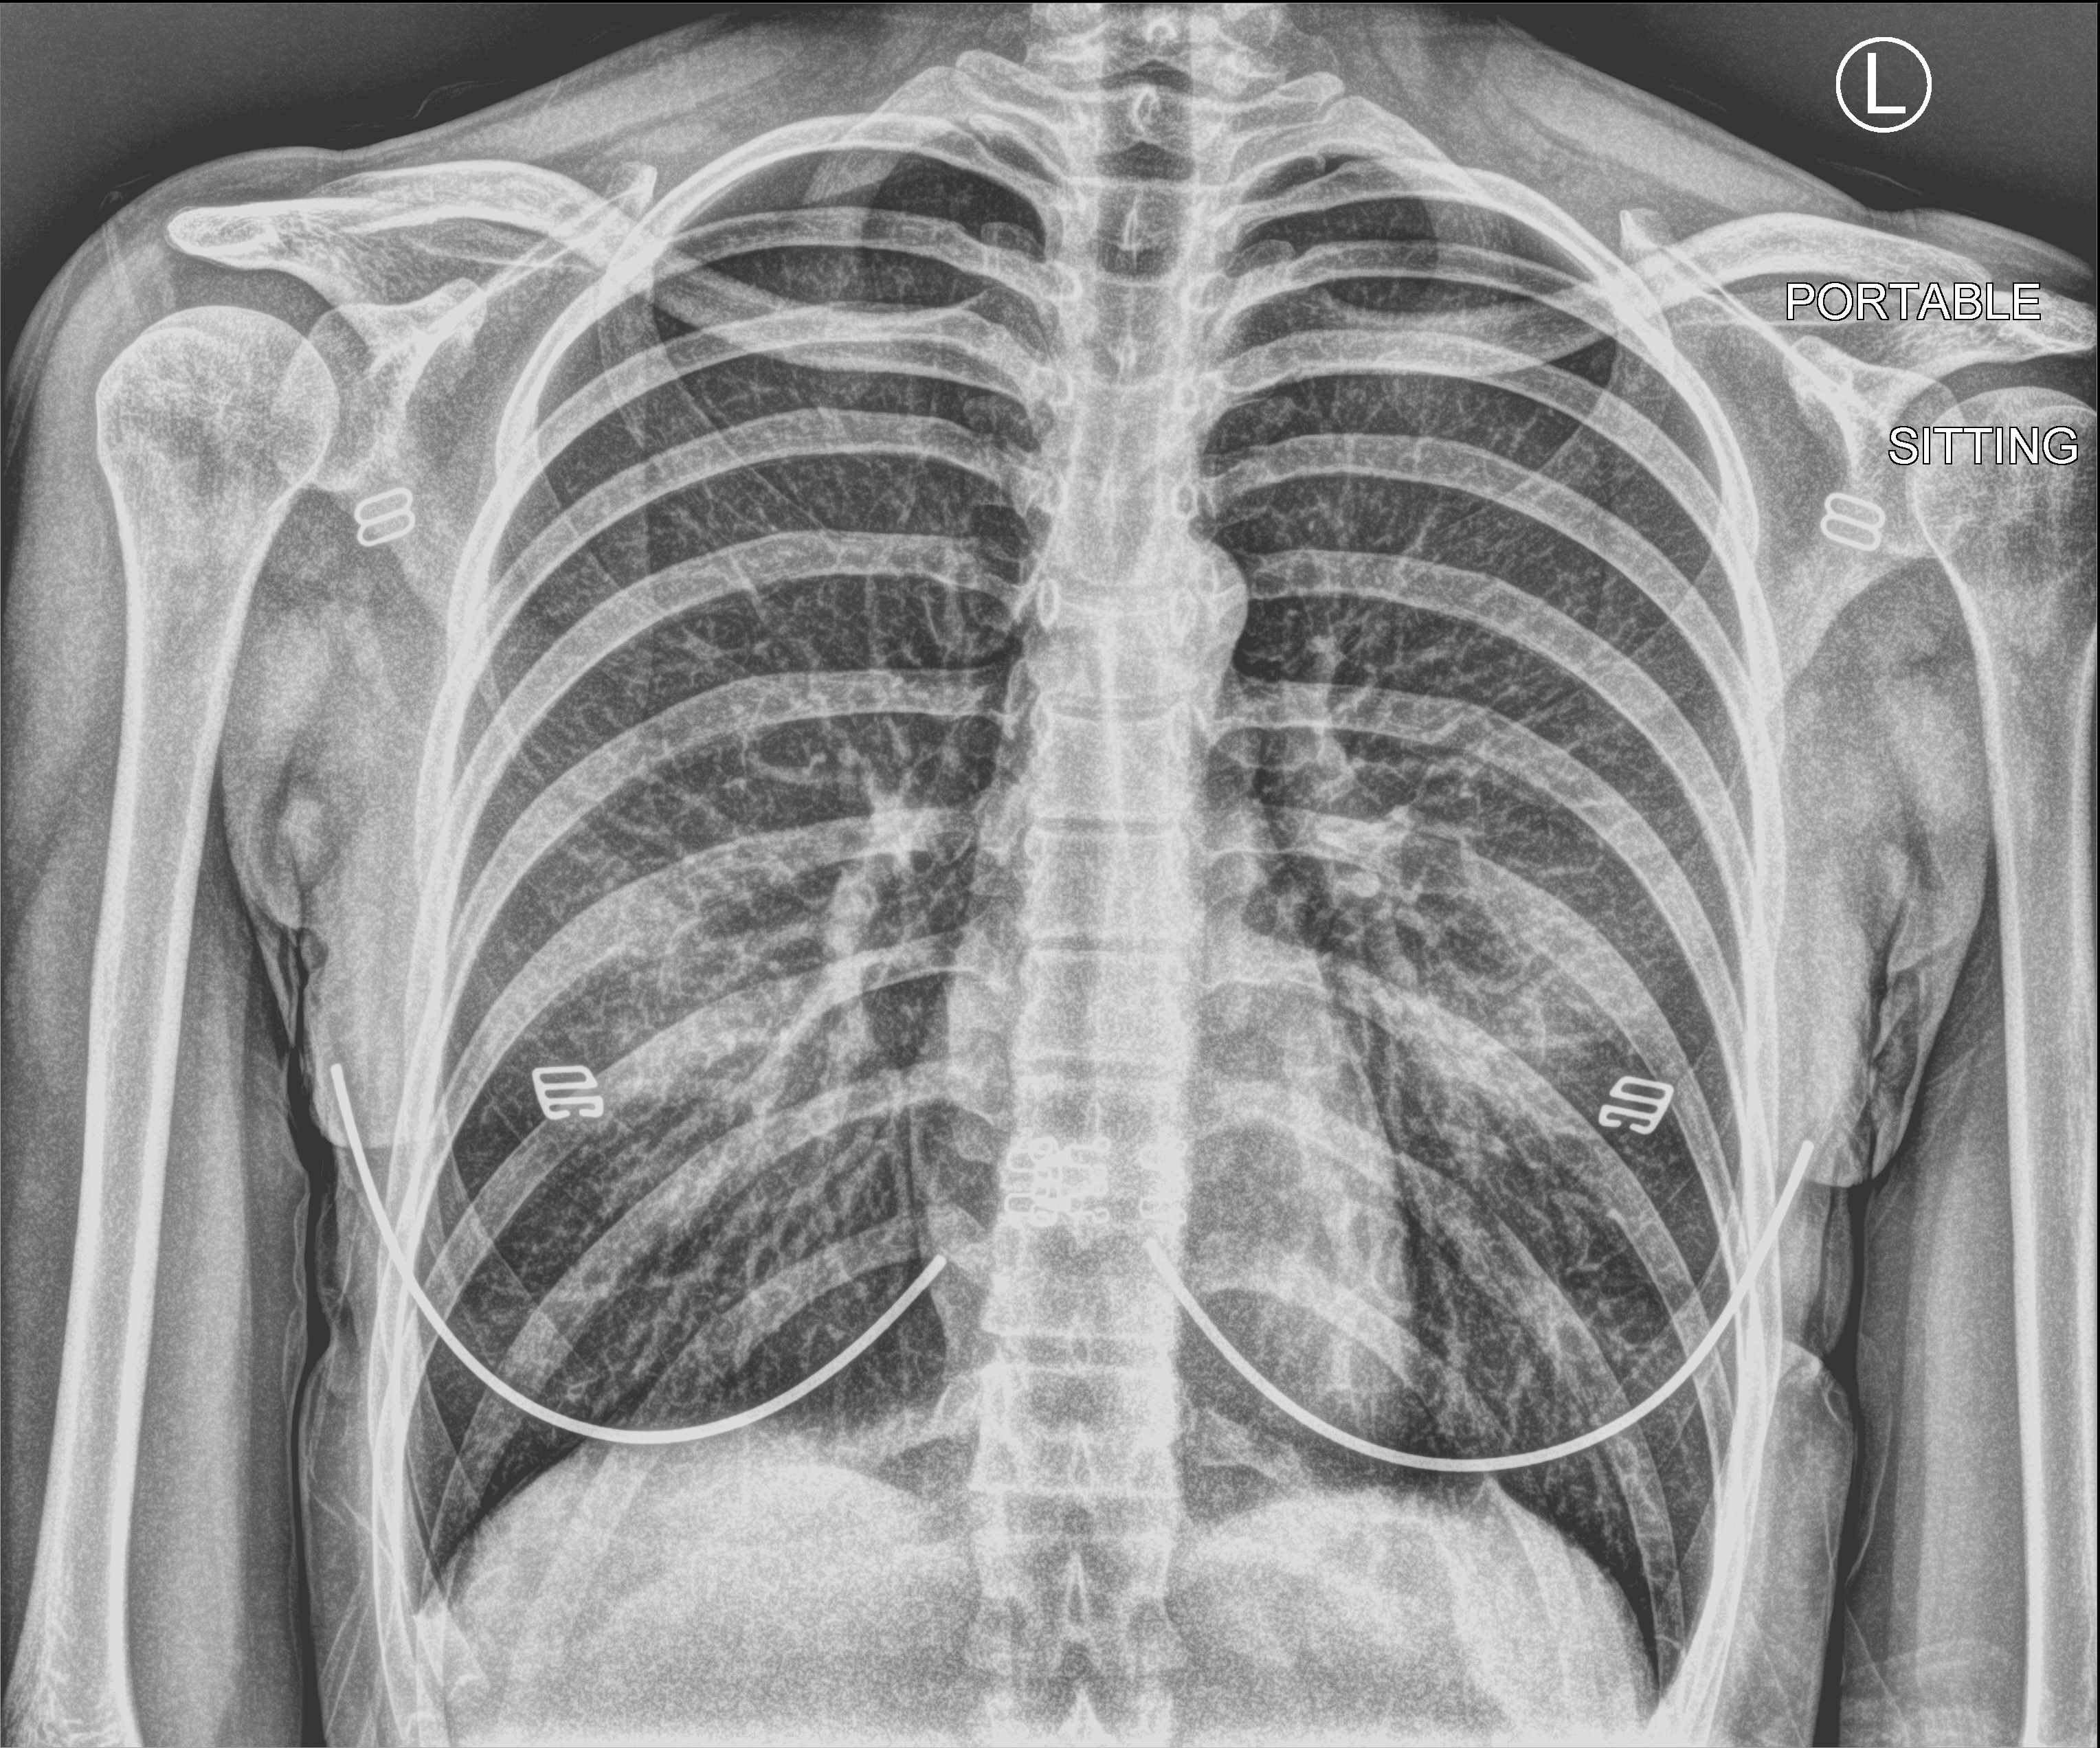
Portable chest radiograph; anteroposterior (AP) projection. Female patient hospitalised with COVID-19, age 18–59 years.
Admission-level facts for this patient (not findings on this image; timing relative to this image not recorded): length of hospital stay: 1 day.